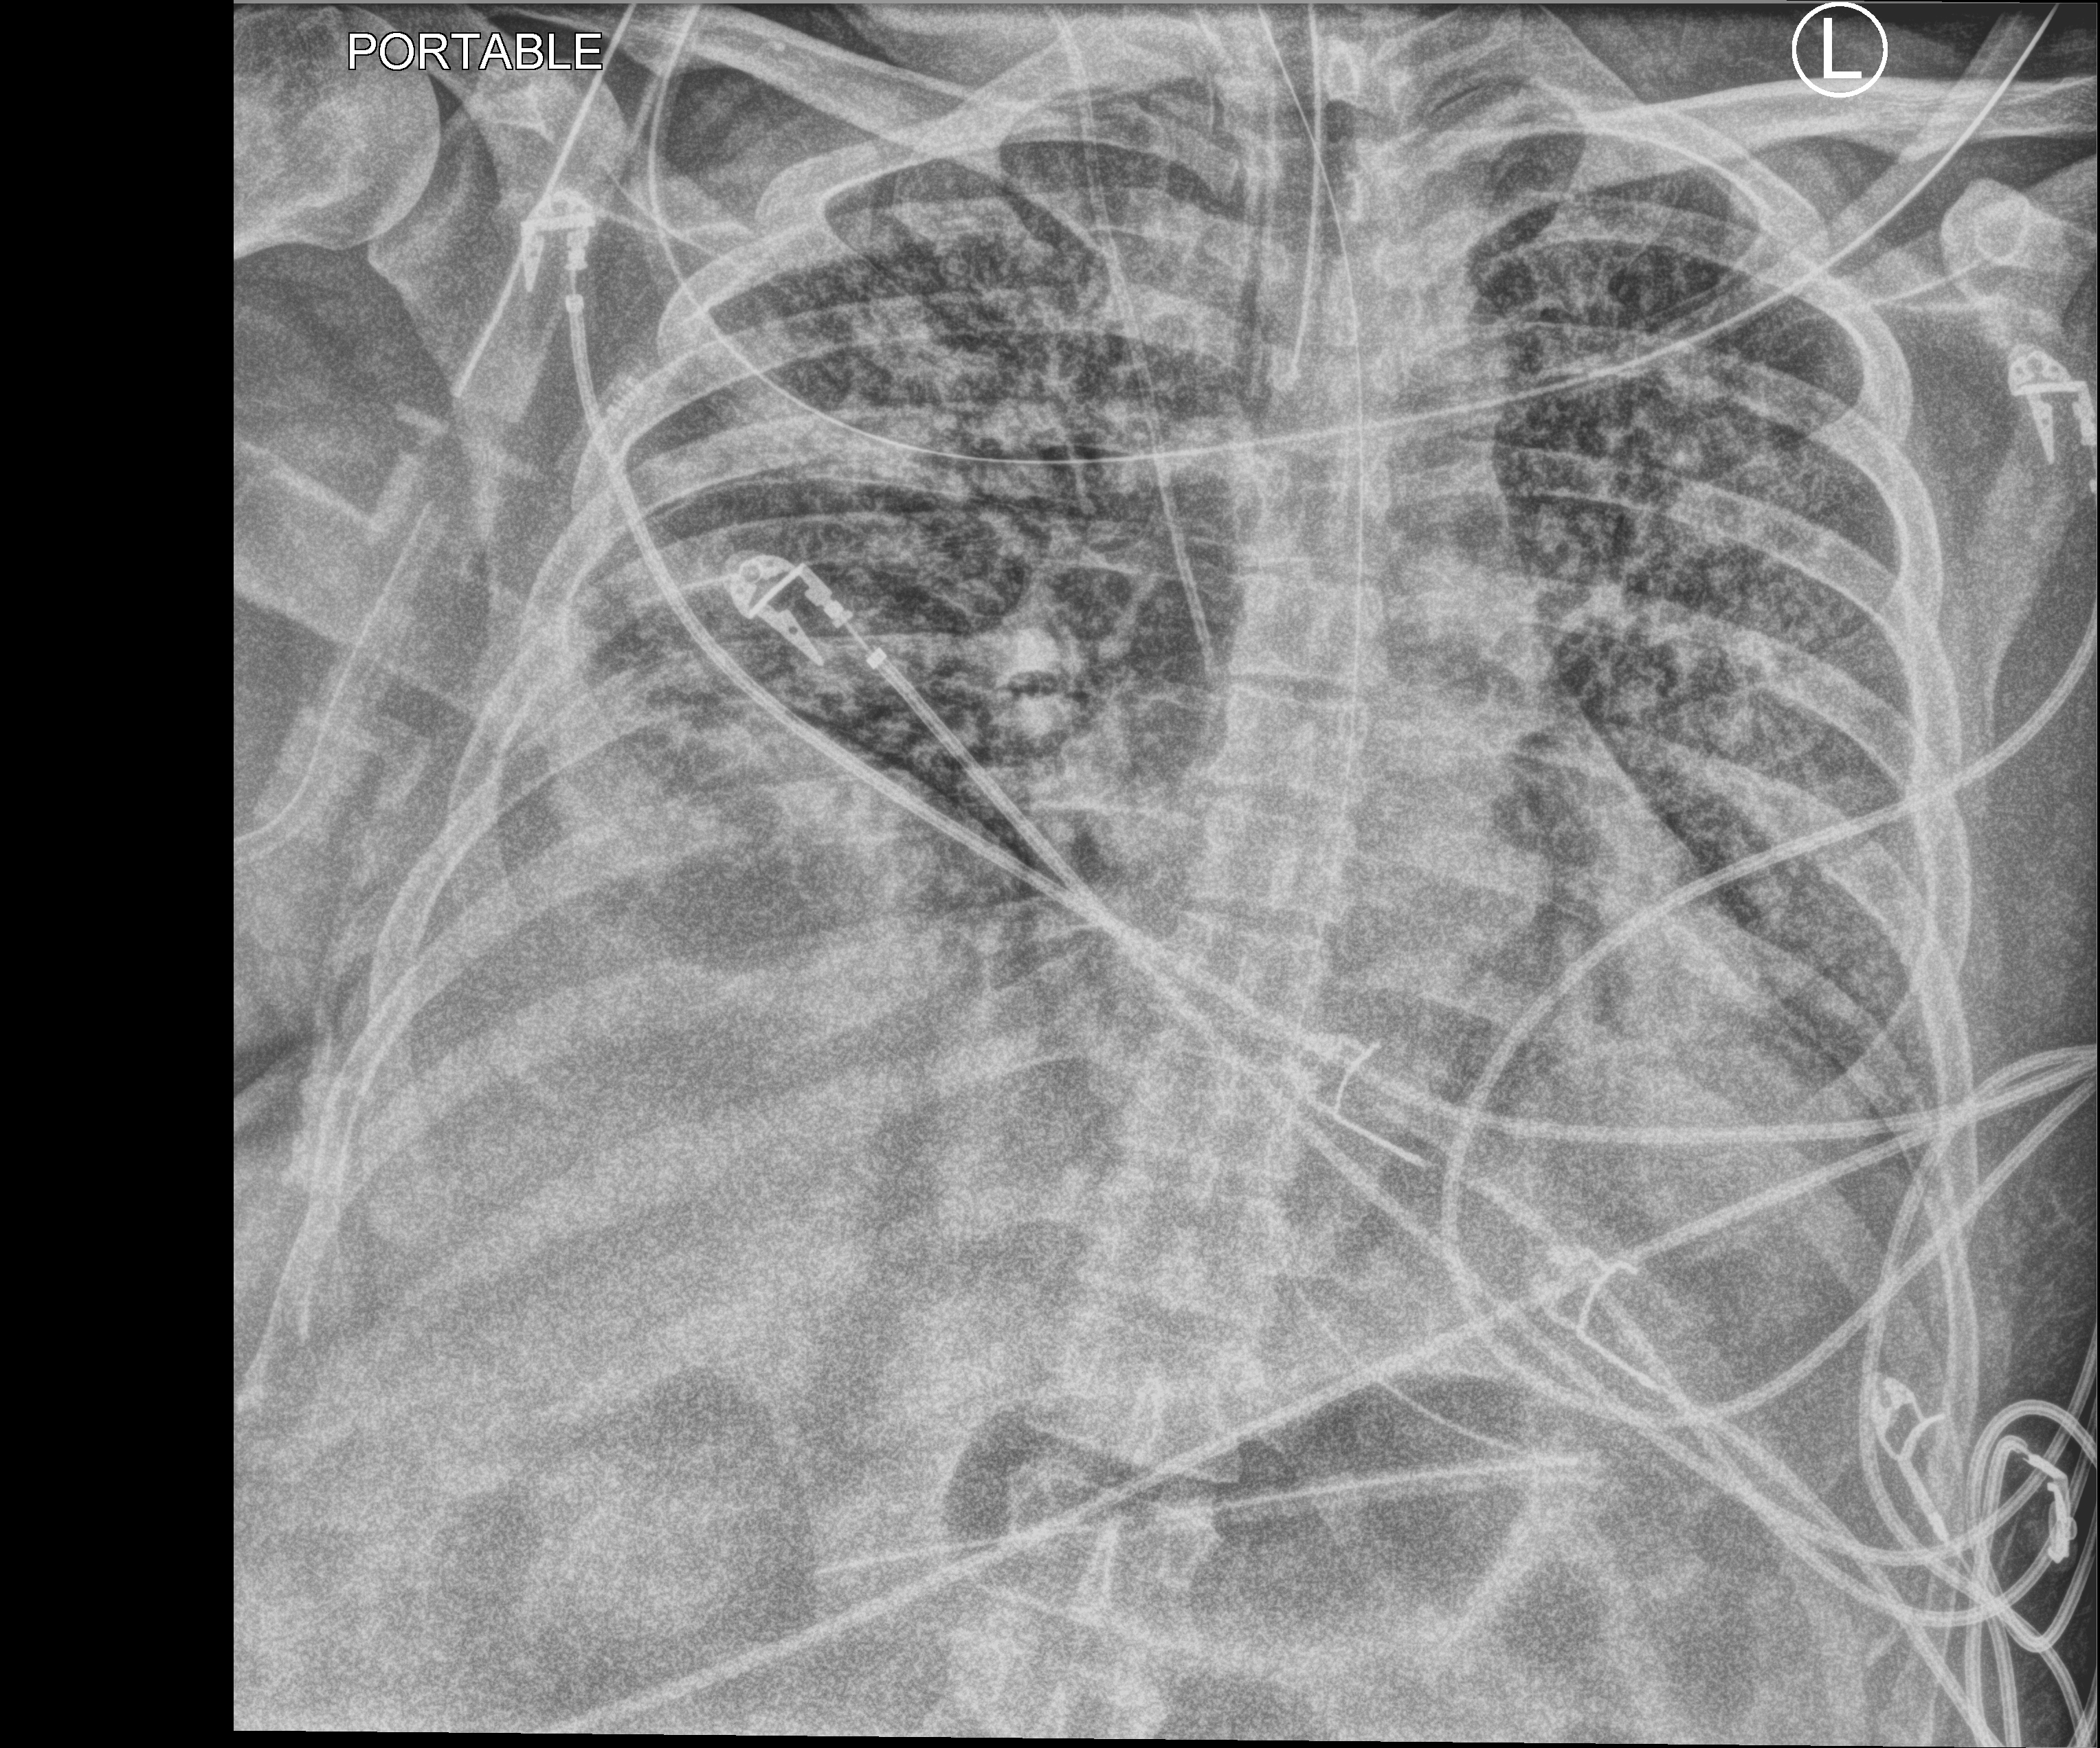
Bedside chest radiograph (computed radiography); anteroposterior (AP) projection. Male patient hospitalised with COVID-19, age 18–59 years.
Hospital-stay facts (about this admission, not read from this image; timing relative to this image not recorded): mechanically ventilated during this hospital stay: yes; admitted to intensive care during this hospital stay: yes; smoking status (admission record): never.